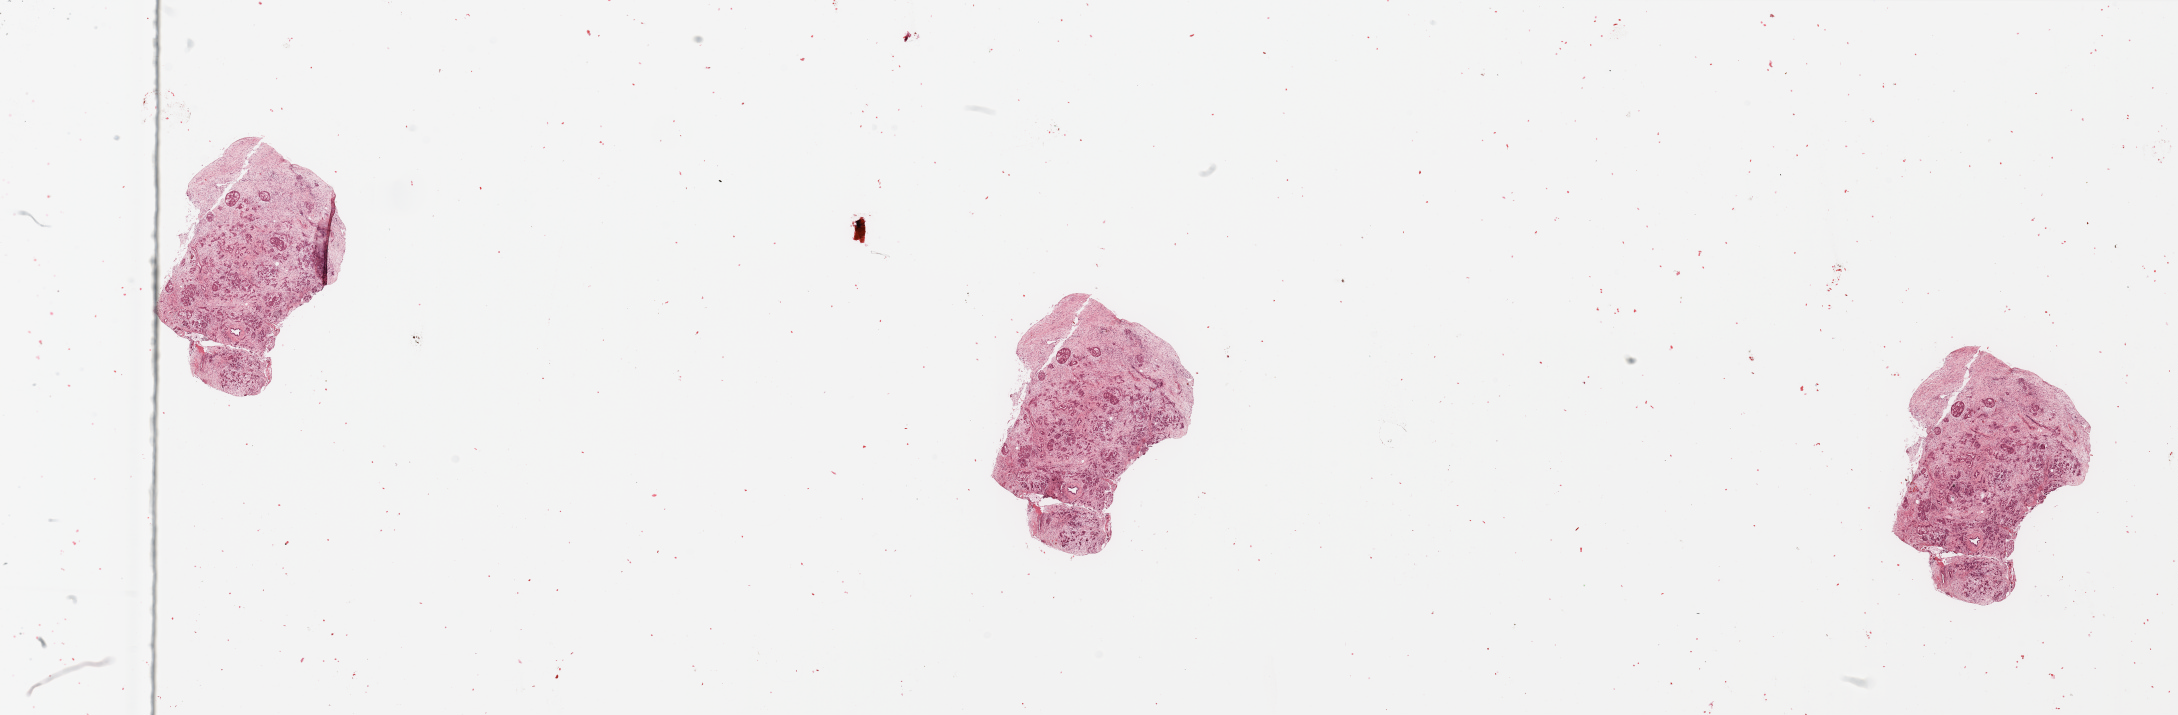
Digitized Hematoxylin and eosin (H&E) stained tissue section (whole slide) — shown as a low-resolution overview of the whole scanned area (about 34.5 x 11.3 mm, acquisition: 20x scan), tumour tissue sample, pancreas. Male, 62 y/o.
* primary tumour site (as recorded): head
* patient diagnosis (cohort enrolment): ductal adenocarcinoma (pancreas)